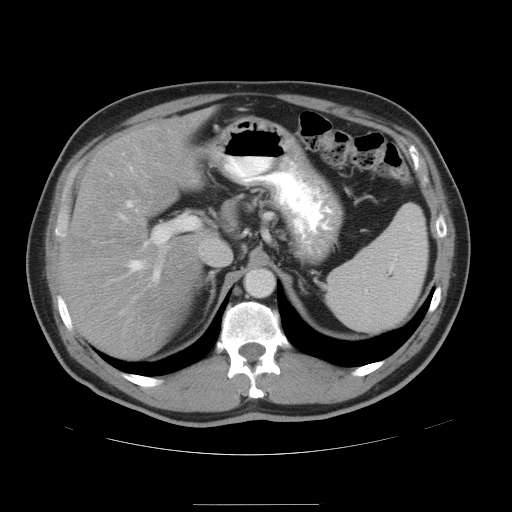
Contrast-enhanced abdominal CT, one axial slice. Position 31 of 47 along the scan axis. 120 kVp. Intravenous contrast given. Soft-tissue window (W 400 / L 40 HU). 512 × 512 image matrix, field of view 420 × 420 mm. Male patient, age 61 years. From the clinical record (not read from this slice): diagnosis: colorectal cancer liver metastases, imaged before liver resection; multiple liver metastases: no; largest metastasis: 1.2 cm.
Annotated regions visible in this slice (expert manual segmentation):
- hepatic veins: bounding box (x1, y1, x2, y2) in pixels: (128, 167, 144, 271)
- liver: (64, 111, 209, 361)
- planned liver remnant (the part of the liver to remain after resection): (64, 111, 209, 361)
- portal vein (with intrahepatic branches): (121, 215, 199, 280)